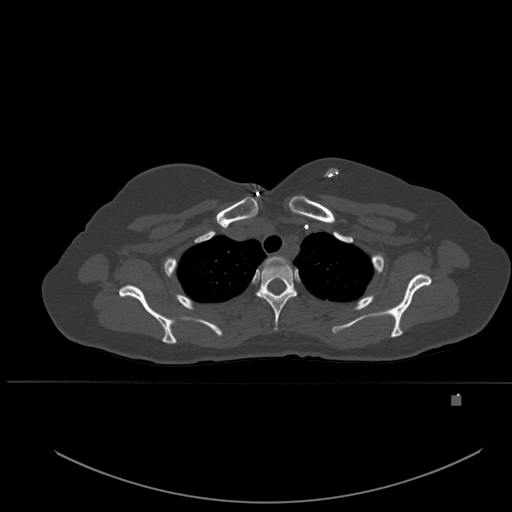
CT including the spine, one axial slice; position 406 of 651 along the scan axis; bone window (W 1800 / L 400 HU); 512 × 512 image matrix, field of view 443 × 443 mm. Patient: female, 49 years. From the clinical record (not read from this slice): primary cancer: breast.
Annotated regions visible in this slice (semi-automatically segmented with operator editing):
- T1 vertebra: bounding box (x1, y1, x2, y2) in pixels: (264, 256, 291, 268)
- T2 vertebra: (257, 259, 297, 331)